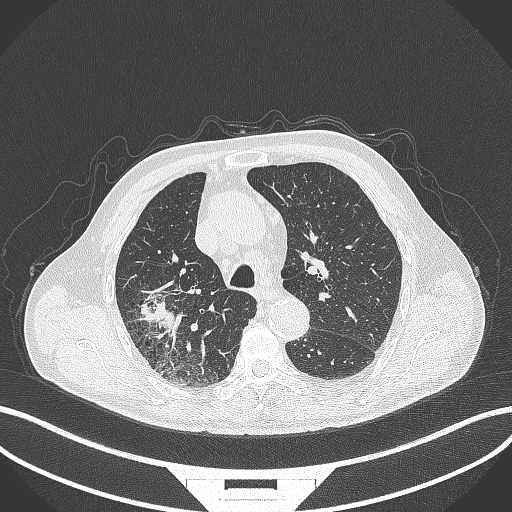
Chest CT, one axial slice; slice 289 of 429 in the series (ordered by position); 120 kVp; lung window (W 1500 / L -600 HU); 1 mm slice thickness; 512 × 512 image matrix, field of view 400 × 400 mm. Male patient, age 72 years. From the clinical record (not read from this slice): clinical TNM (as recorded): T3 N2 M0.
Structures marked on this image (bounding box drawn by a radiologist):
- lung tumour (recorded histology: adenocarcinoma): bounding box (x1, y1, x2, y2) in pixels: (133, 286, 188, 357)